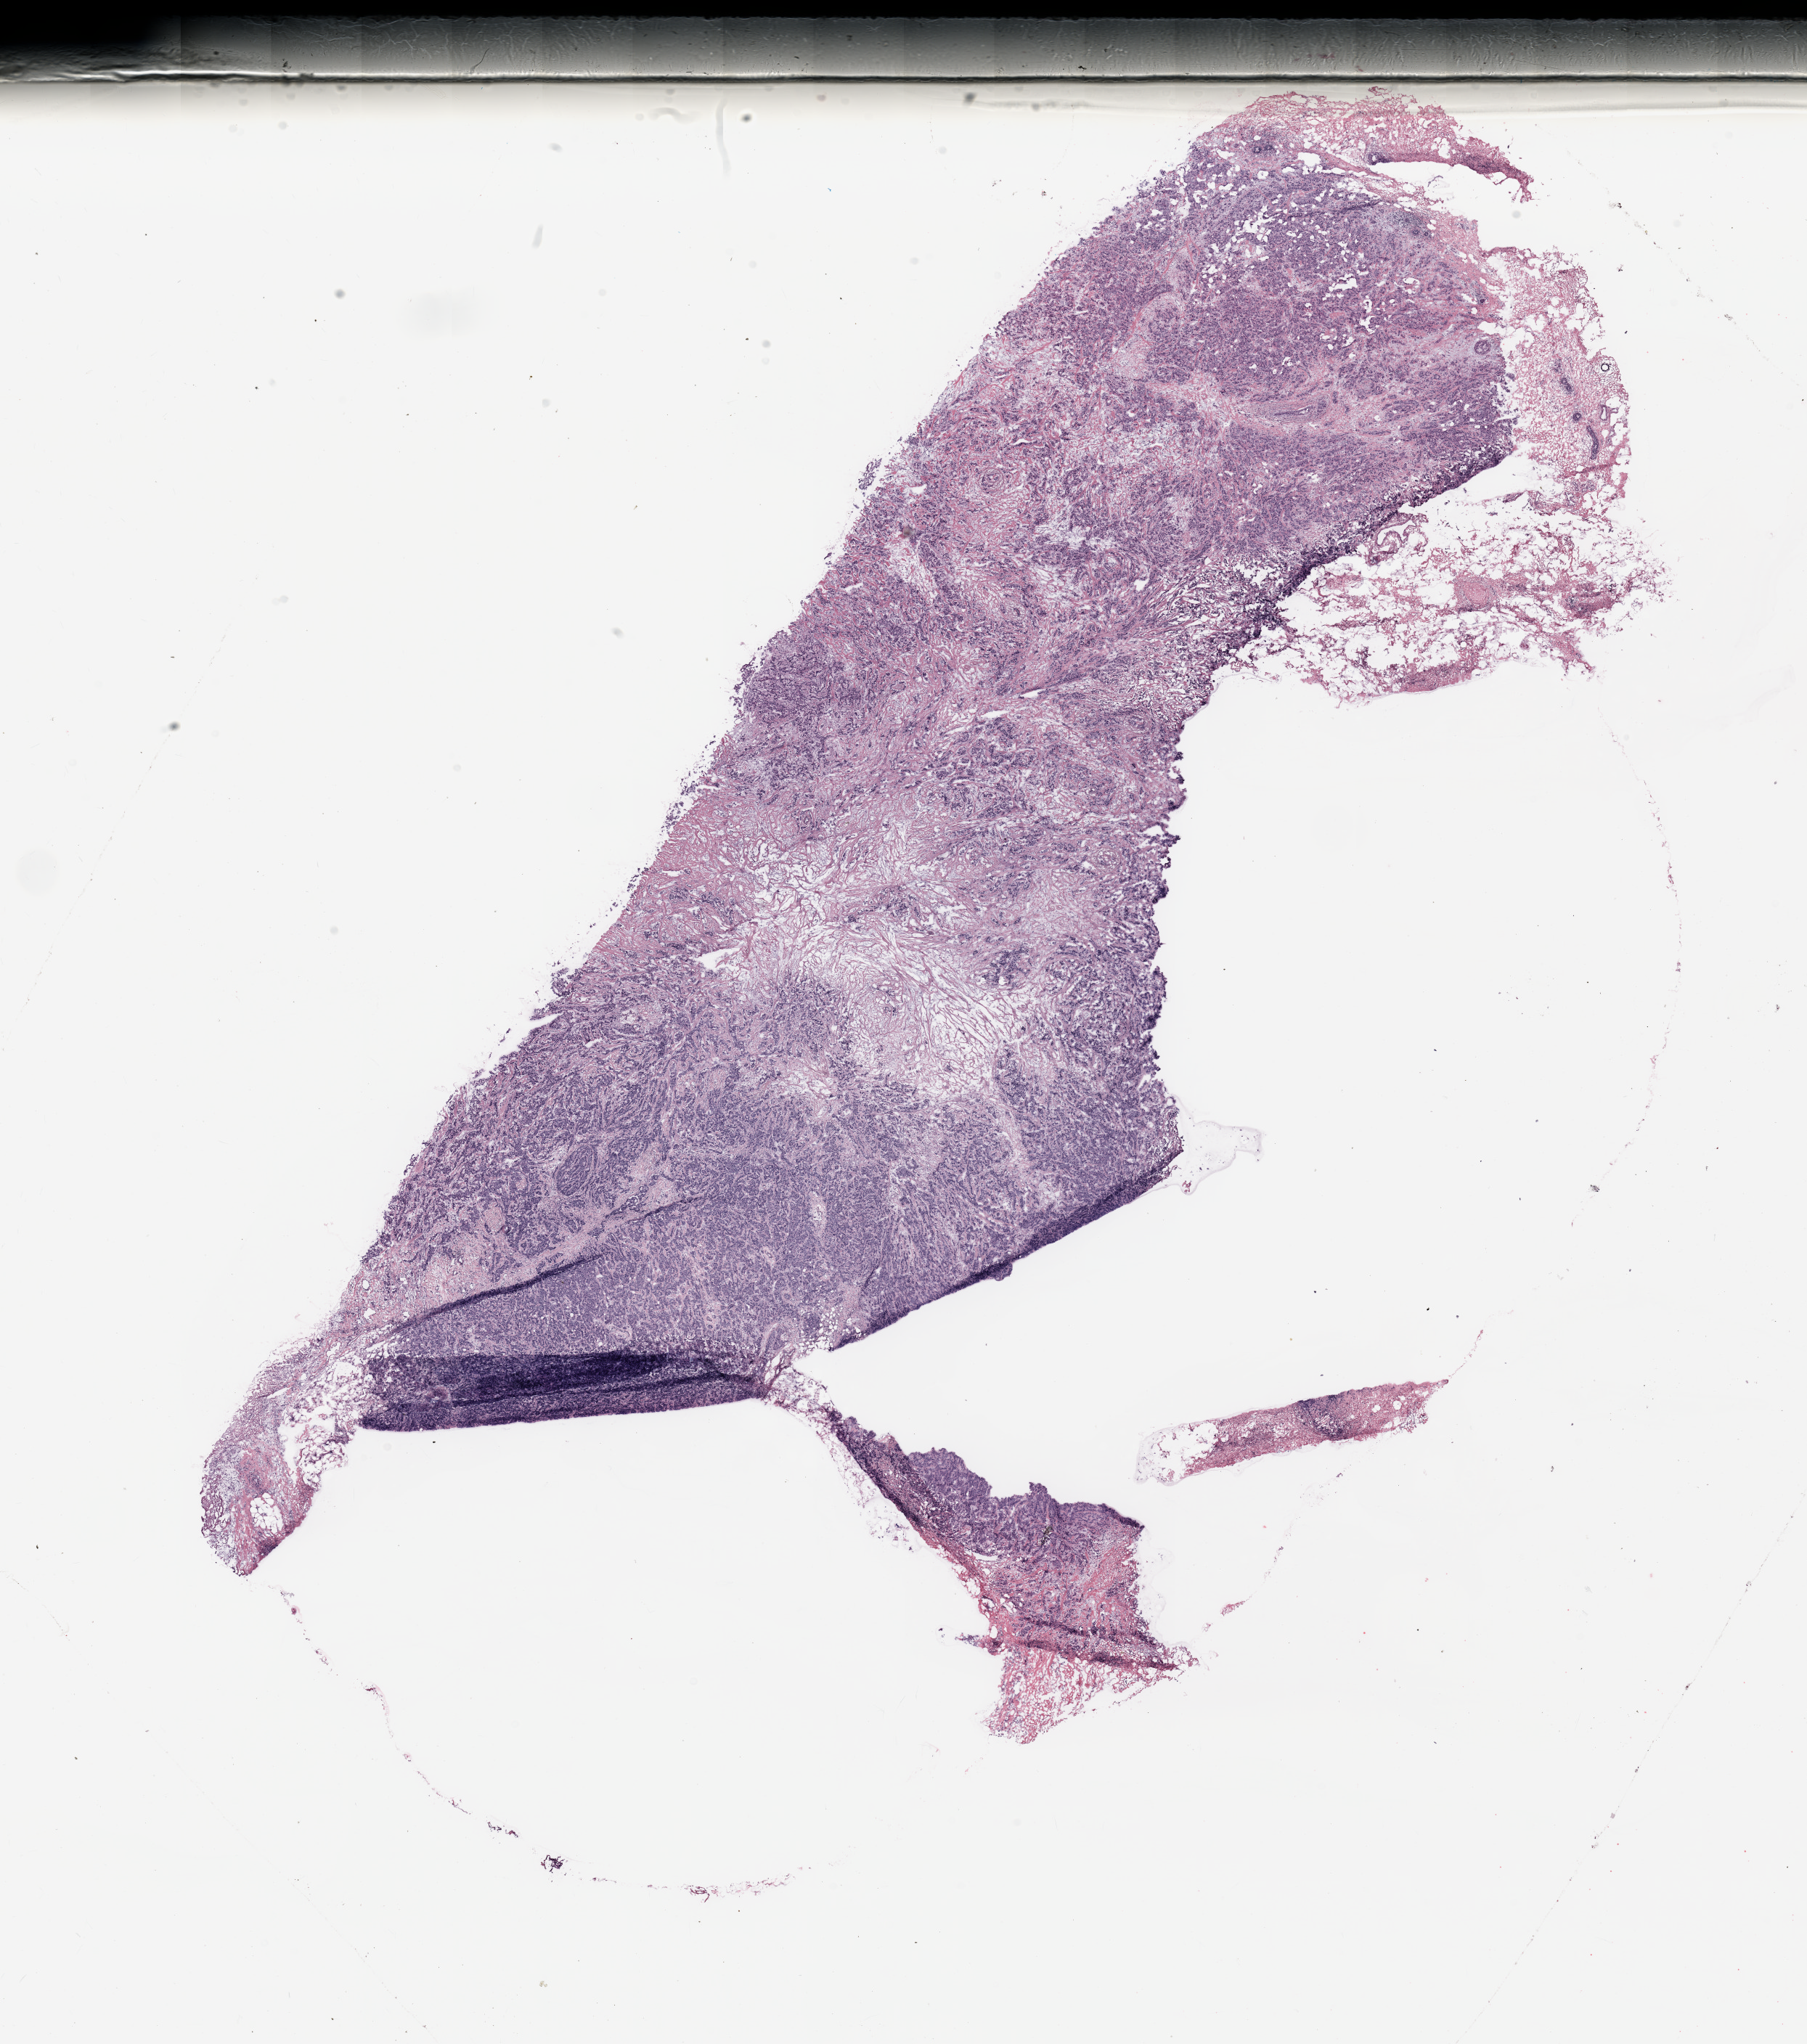
Whole-slide histology image, H&E, shown as a low-resolution overview of the whole scanned area (about 19.7 x 22.3 mm, acquisition: 20x scan), tumour tissue sample, breast. Female, 55 y/o.
Diagnosis: Infiltrating duct carcinoma, NOS. AJCC pathologic stage: IIA.